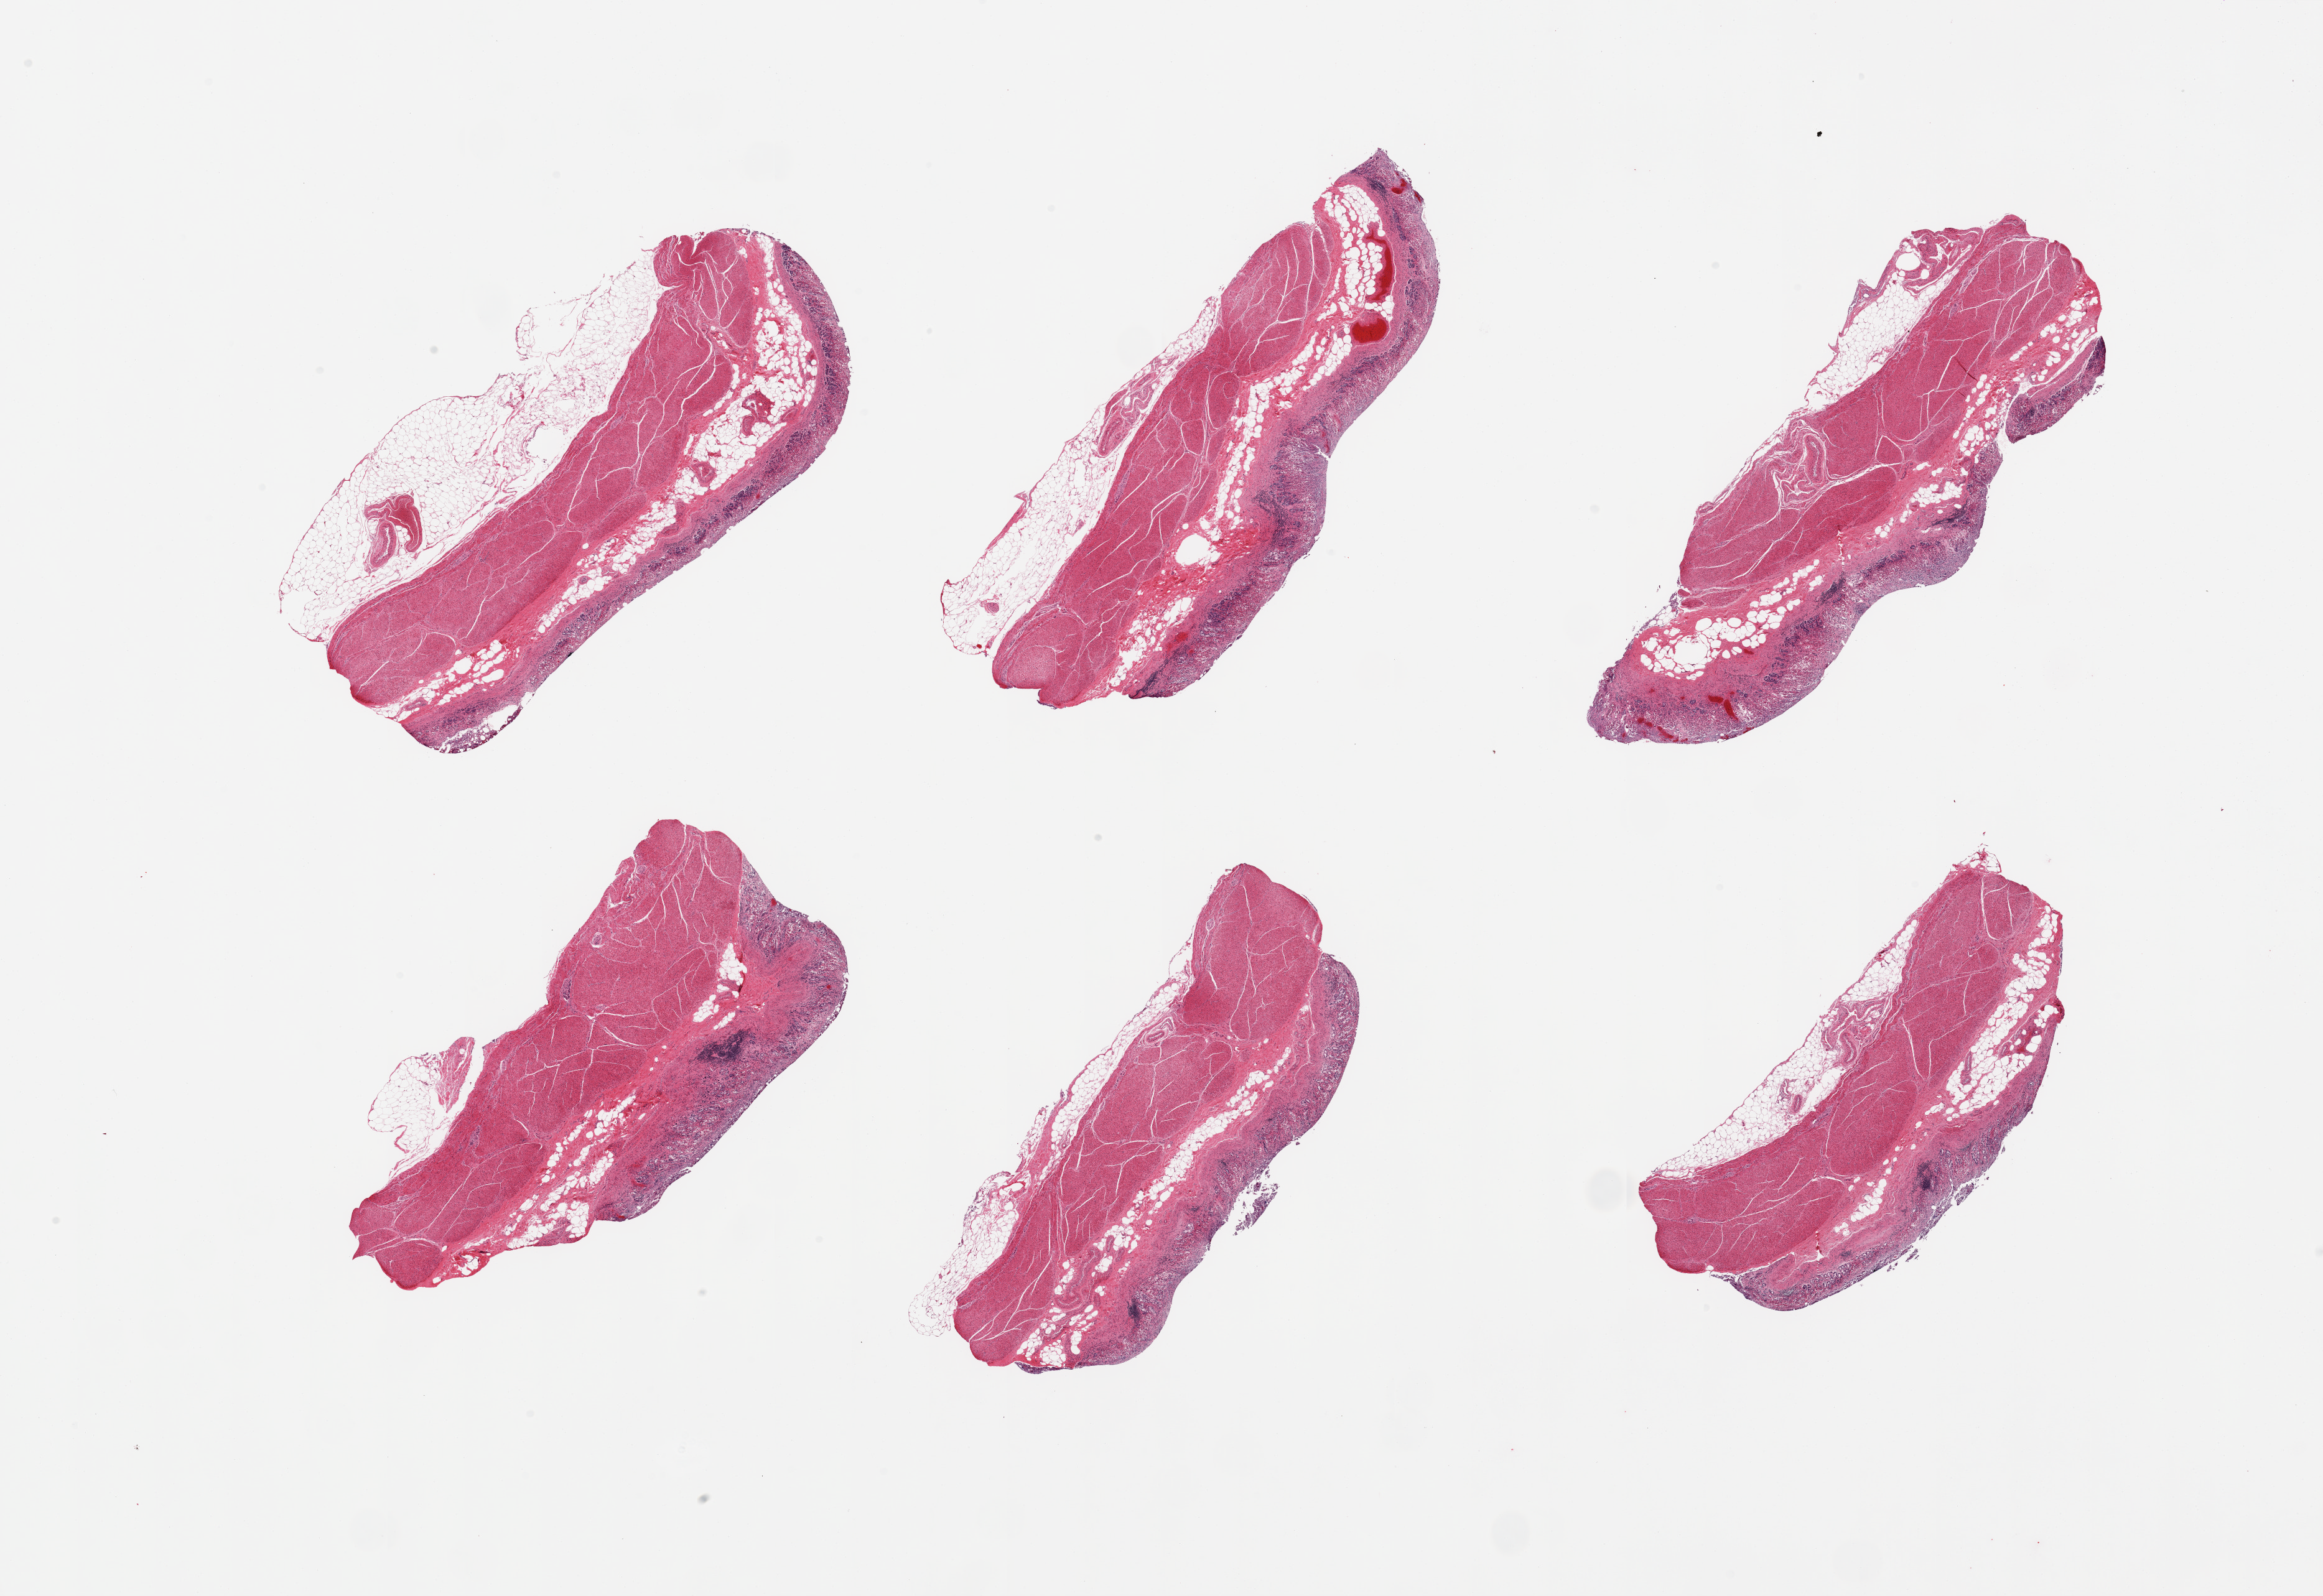
Haematoxylin and eosin whole-slide image, shown as a low-resolution overview of the whole scanned area (about 29.5 x 20.3 mm, acquisition: 20x scan). PAXgene-fixed, paraffin-embedded tissue. Sampled site (target tissue): stomach. Donor tissue sample. Donor sex: male.
- review note (as recorded): 6 pieces; full thickness sections with autolyzed mucosa; attached fat up to 1.6mm; congestion